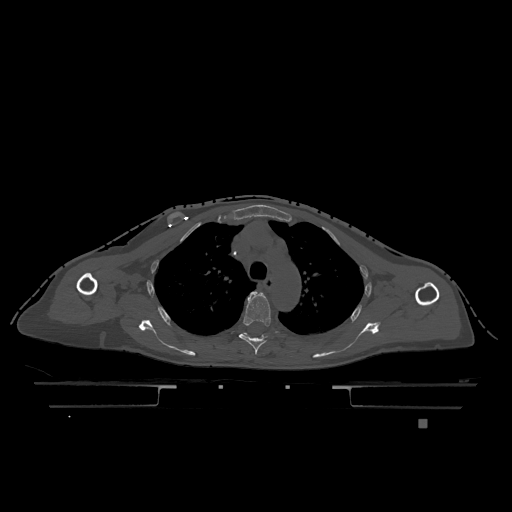
CT including the spine, one axial slice; position 877 of 1317 along the scan axis; bone window (W 1800 / L 400 HU); 0.5 mm slice thickness; 512 × 512 image matrix, field of view 500 × 500 mm. Female patient, age 74 years. From the clinical record (not read from this slice): primary cancer: lung; vertebrae with lytic lesions (as recorded): T1, T4, T5, T6, L4, L5.
Structures marked on this image (semi-automatically segmented with operator editing):
- T4 vertebra: box from (x=239, y=291) to (x=274, y=355) px
- T5 vertebra: (x=244, y=333)–(x=247, y=335)